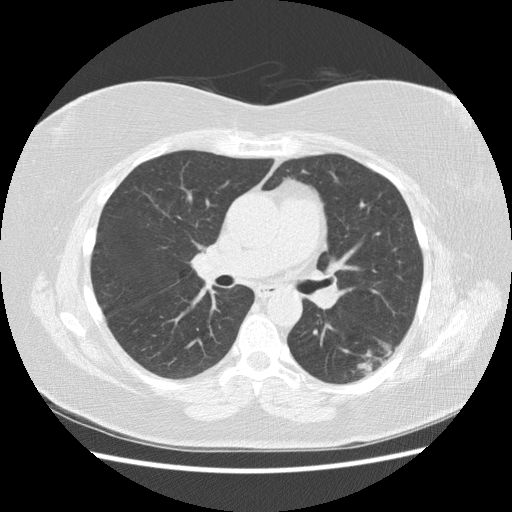
Low-dose screening chest CT, axial slice; third screening round (two years after baseline); lung window (W 1500 / L -600 HU); 2.5 mm slice thickness; 512 × 512 image matrix, field of view 360 × 360 mm. Female, age 57 years at enrolment. Current smoker at enrolment.
- Lesion marked by an expert reader, bounding box [x1, y1, x2, y2] px = [330, 326, 413, 387].
- The exam's reader record, not a measurement of the box and not confirmed to be the same lesion: non-calcified nodule or mass ≥4 mm, left lower lobe, 40 × 20 mm, poorly defined margins, mixed attenuation, pre-existing on the prior screen: yes; interval growth: yes.
- Later outcome: lung cancer diagnosed 55 days after this screen — squamous cell carcinoma, NOS, left lower lobe, poorly differentiated (G3), stage IB (AJCC 6th edition), 40 mm at pathology.